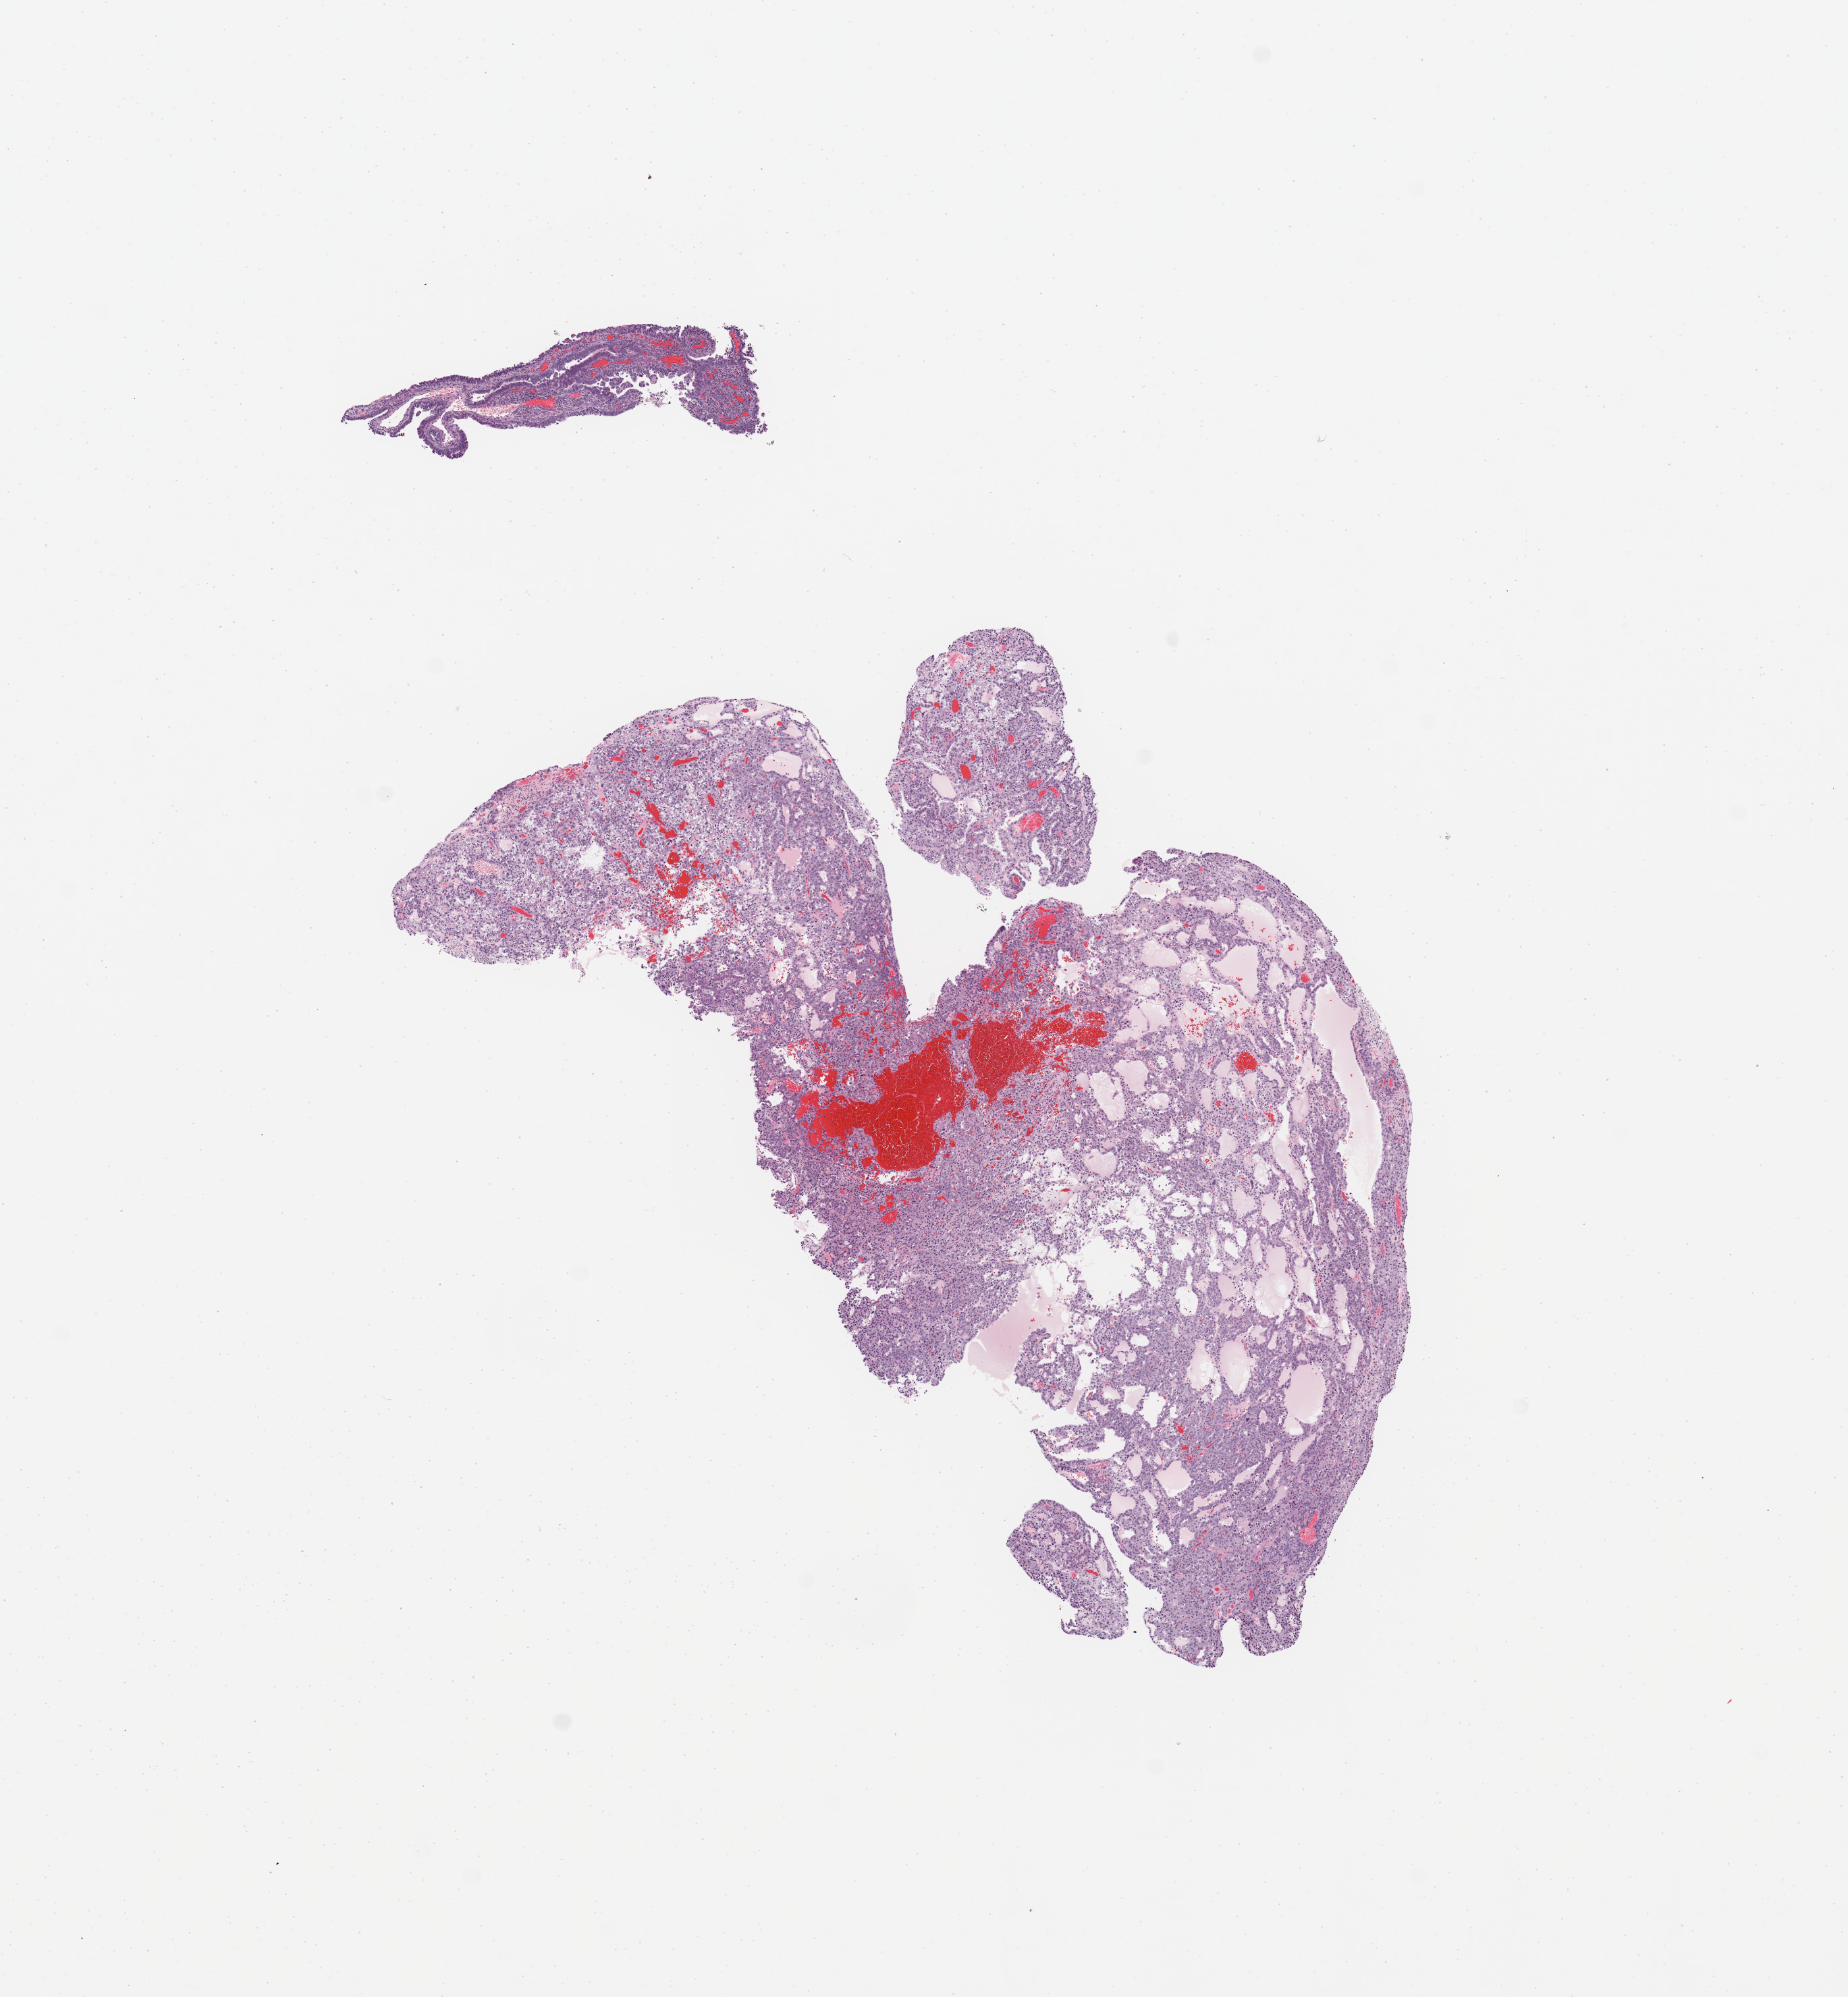
H&E-stained whole-slide image, a low-resolution overview of the entire scanned area, about 10.8 x 11.7 mm. Tumour tissue sample, sampled site: uterus. 60-year-old female patient. Pathologist review of this section (percent, as recorded): tumour nuclei 90%, necrosis 2%.
Histologic diagnosis: Endometrioid adenocarcinoma, NOS.